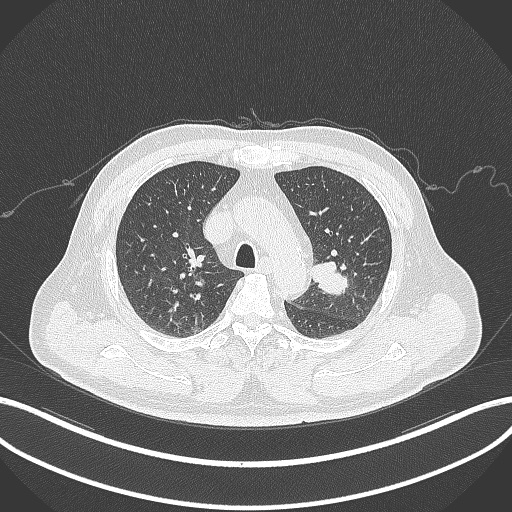
Chest CT, one axial slice. Slice 221 of 286 in the series (ordered by position). 120 kVp. Lung window (W 1500 / L -600 HU). 512 × 512 image matrix. Male patient, age 67 years. Case-level facts recorded for this patient, not image findings: clinical TNM (as recorded): T2a N1 M0.
Outlined on this slice (bounding box drawn by a radiologist):
- lung tumour (recorded histology: adenocarcinoma): bounding box <310,260,351,298> (left, top, right, bottom; pixels)